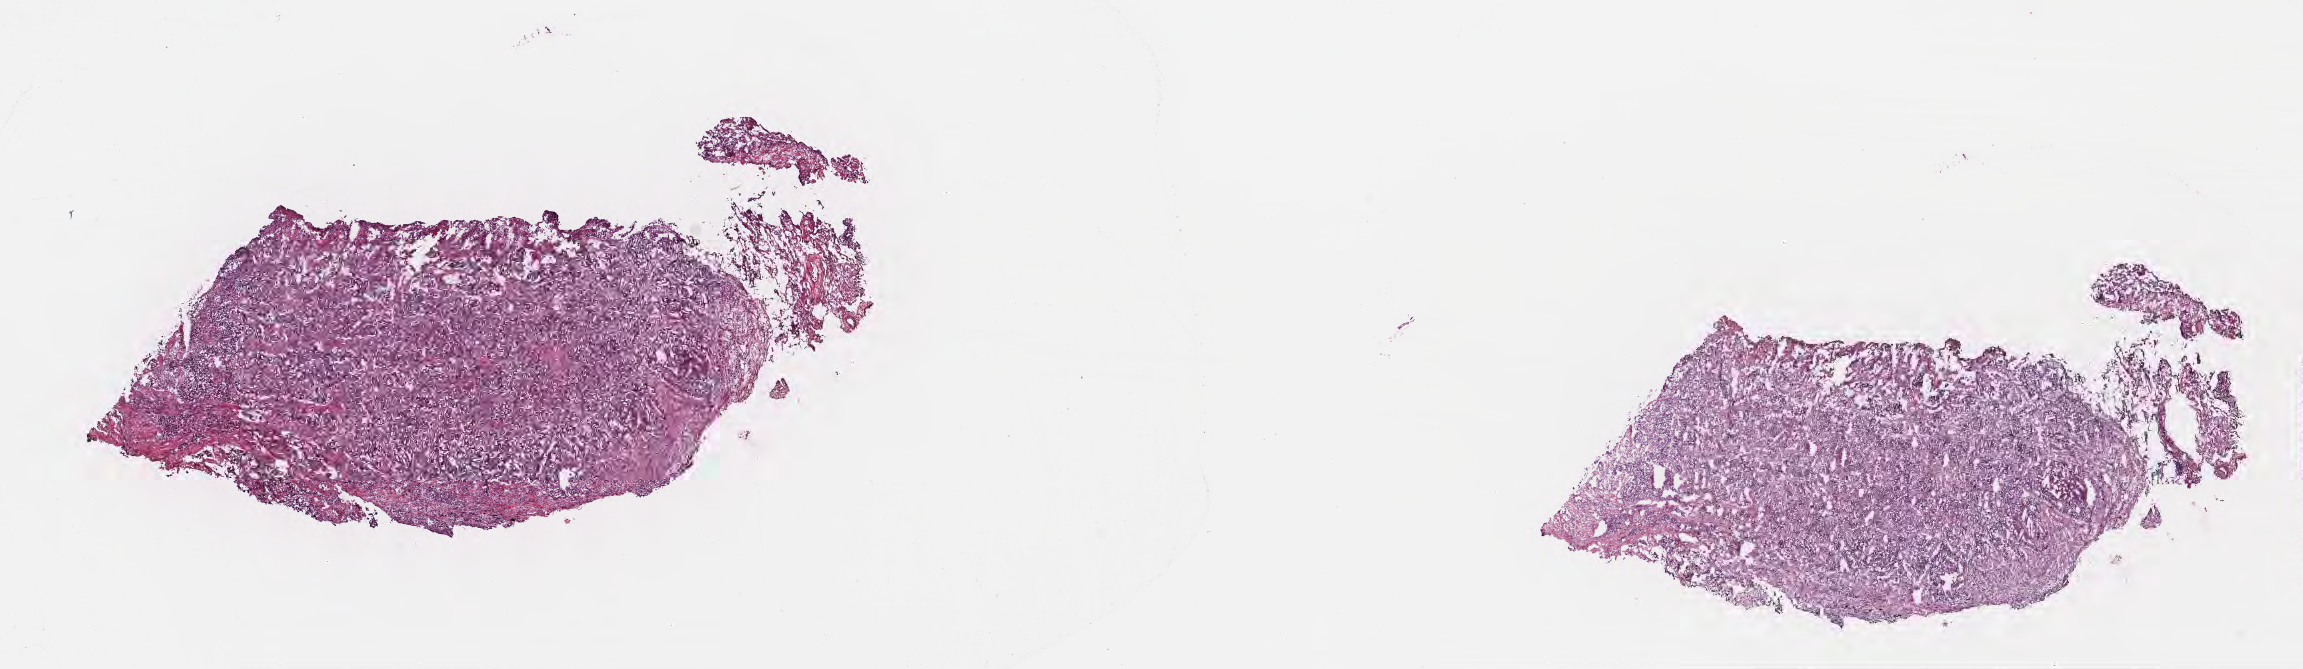
Haematoxylin and eosin whole-slide image, whole scanned area (about 18.6 x 5.4 mm) shown as a low-resolution overview. Frozen section. Primary tumor. Anatomic site: upper lobe of right lung. Patient female; age 74 years. Pathologist review of this section (percent, as recorded): tumor cells 40%, tumor nuclei 60%, stromal cells 55%, necrosis 5%, normal cells 0%. Inflammatory infiltration, as recorded: lymphocyte infiltration 0%, monocyte infiltration 0%, neutrophil infiltration 0%.
• section: top of the tissue portion
• AJCC pathologic stage: Stage IIA
• diagnosis: Adenocarcinoma, NOS